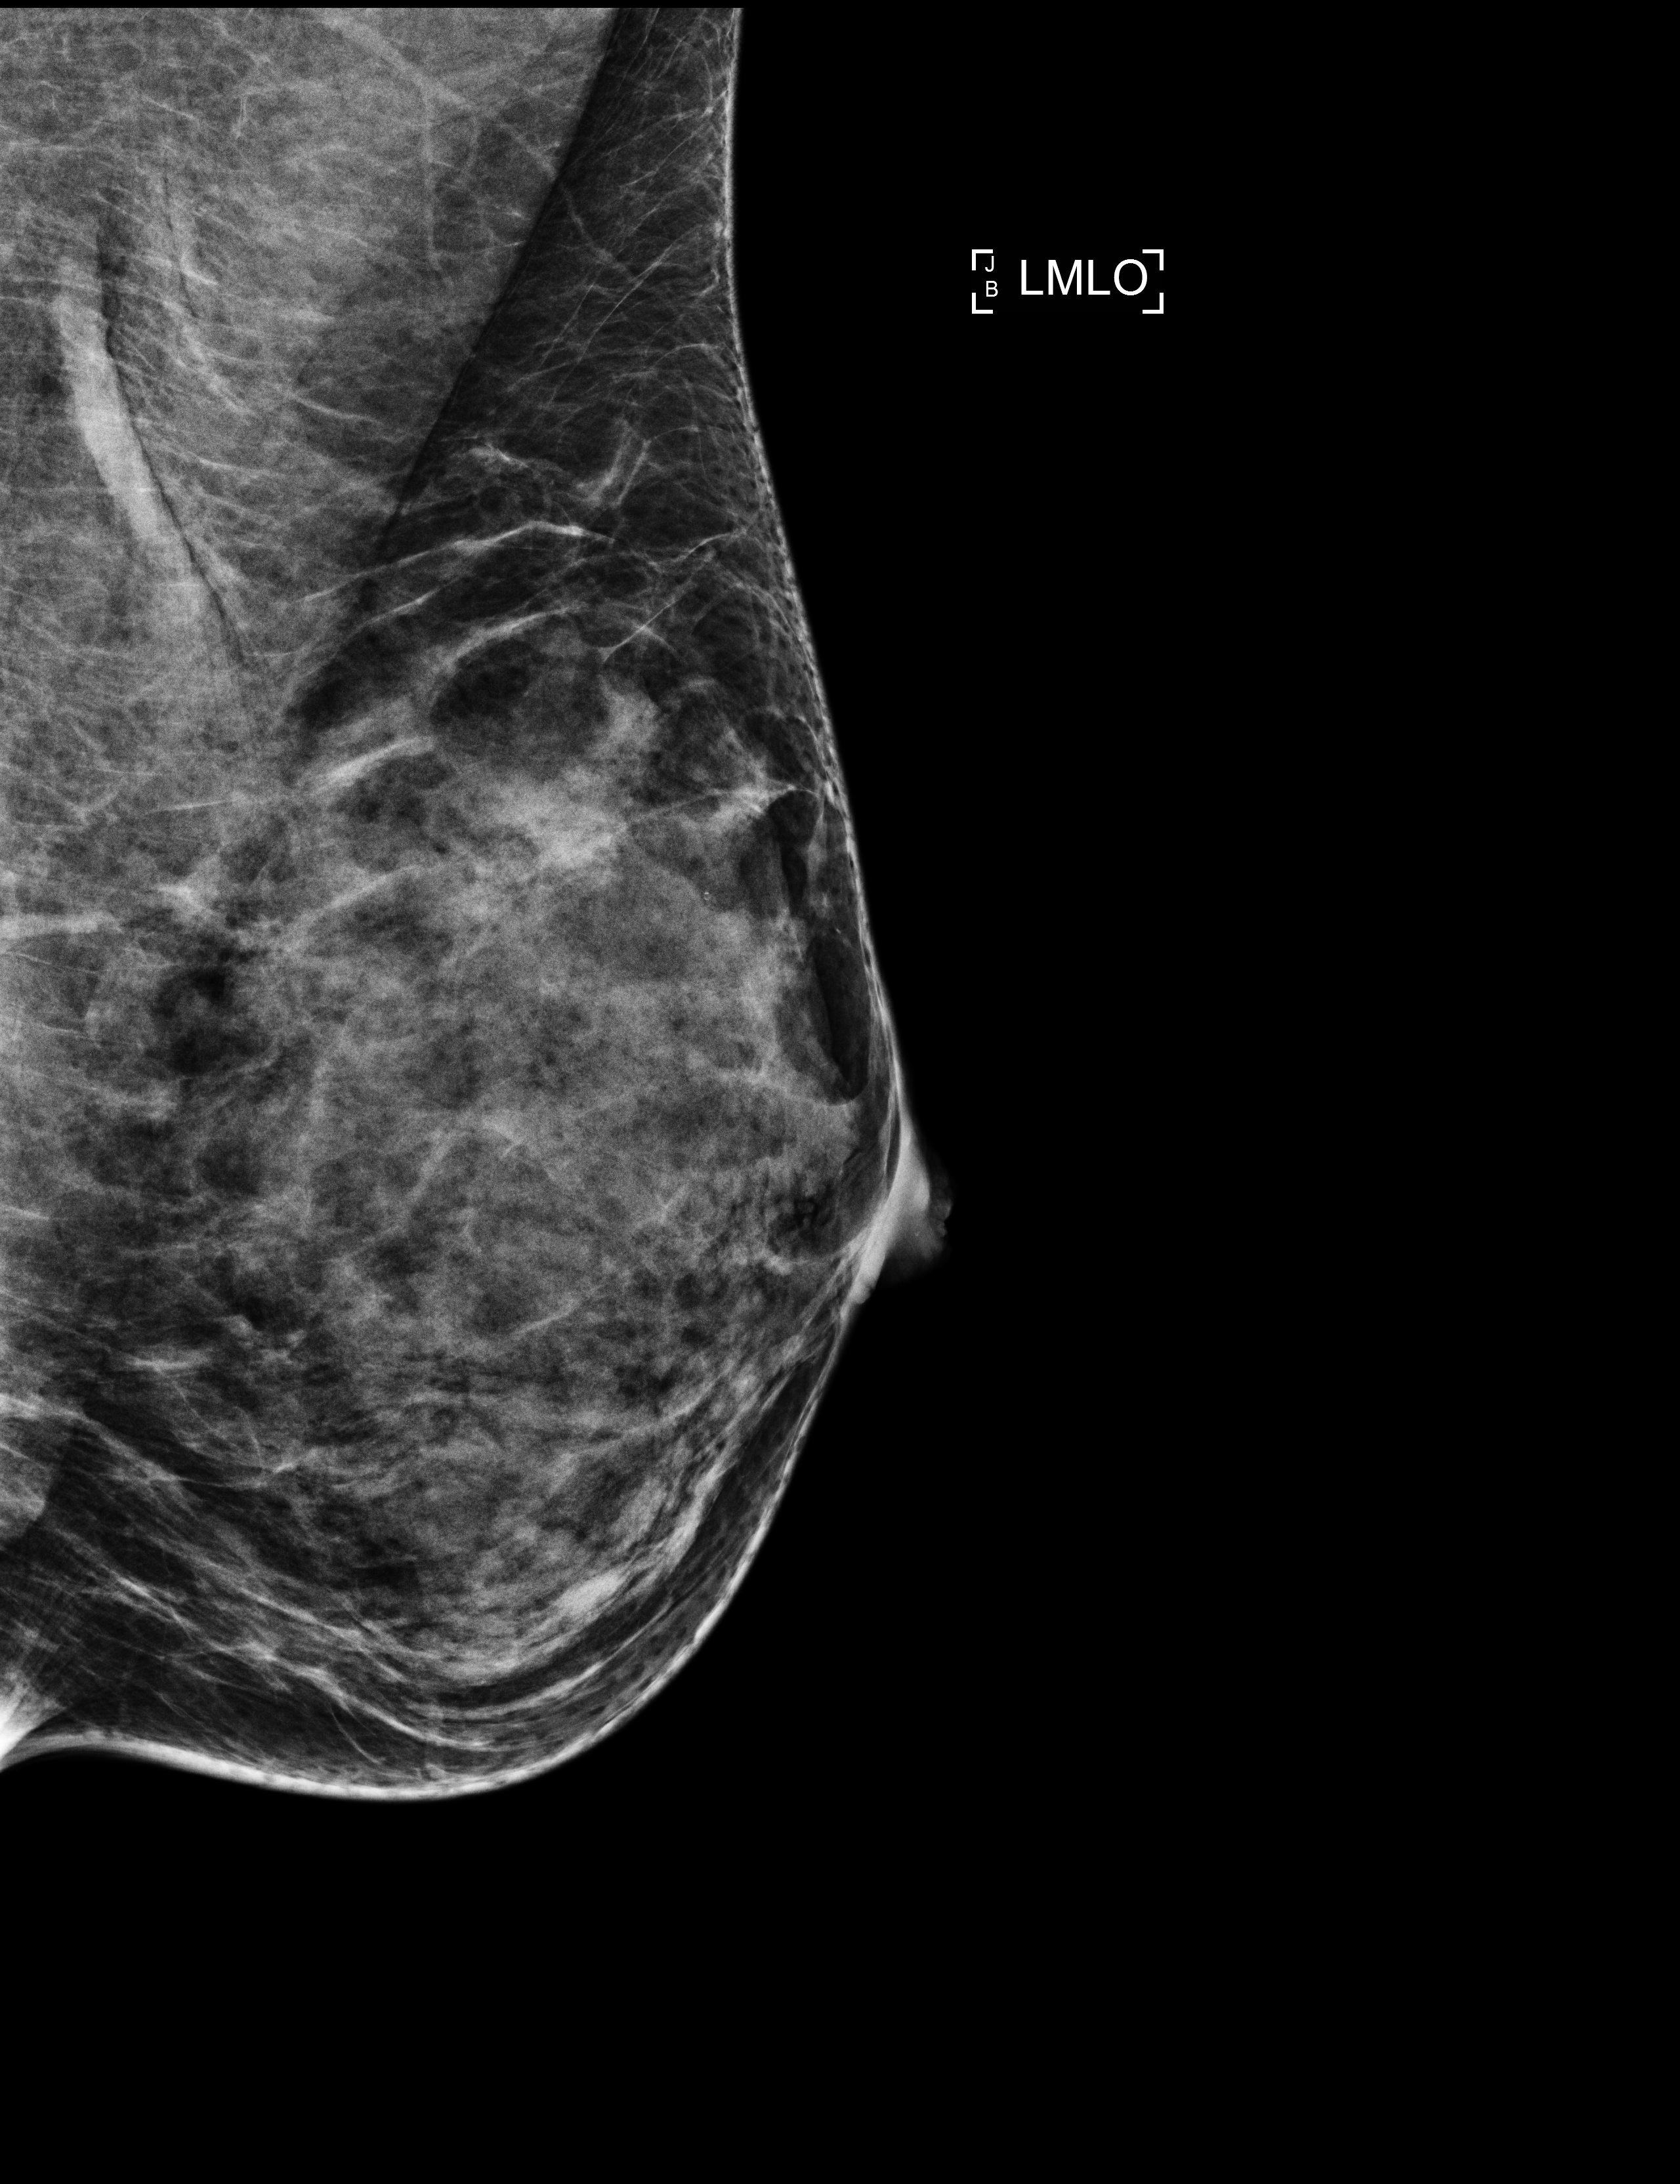
Digital mammogram (FFDM); left breast; mediolateral oblique (MLO) view; annual screening mammography examination. Patient: female, 46 years.
Breast density at the screening exam (both breasts): extremely dense (BI-RADS density category d). Final BI-RADS category for the screening round (tomosynthesis exam, both breasts): category 1. Recall: no recall after this screen.